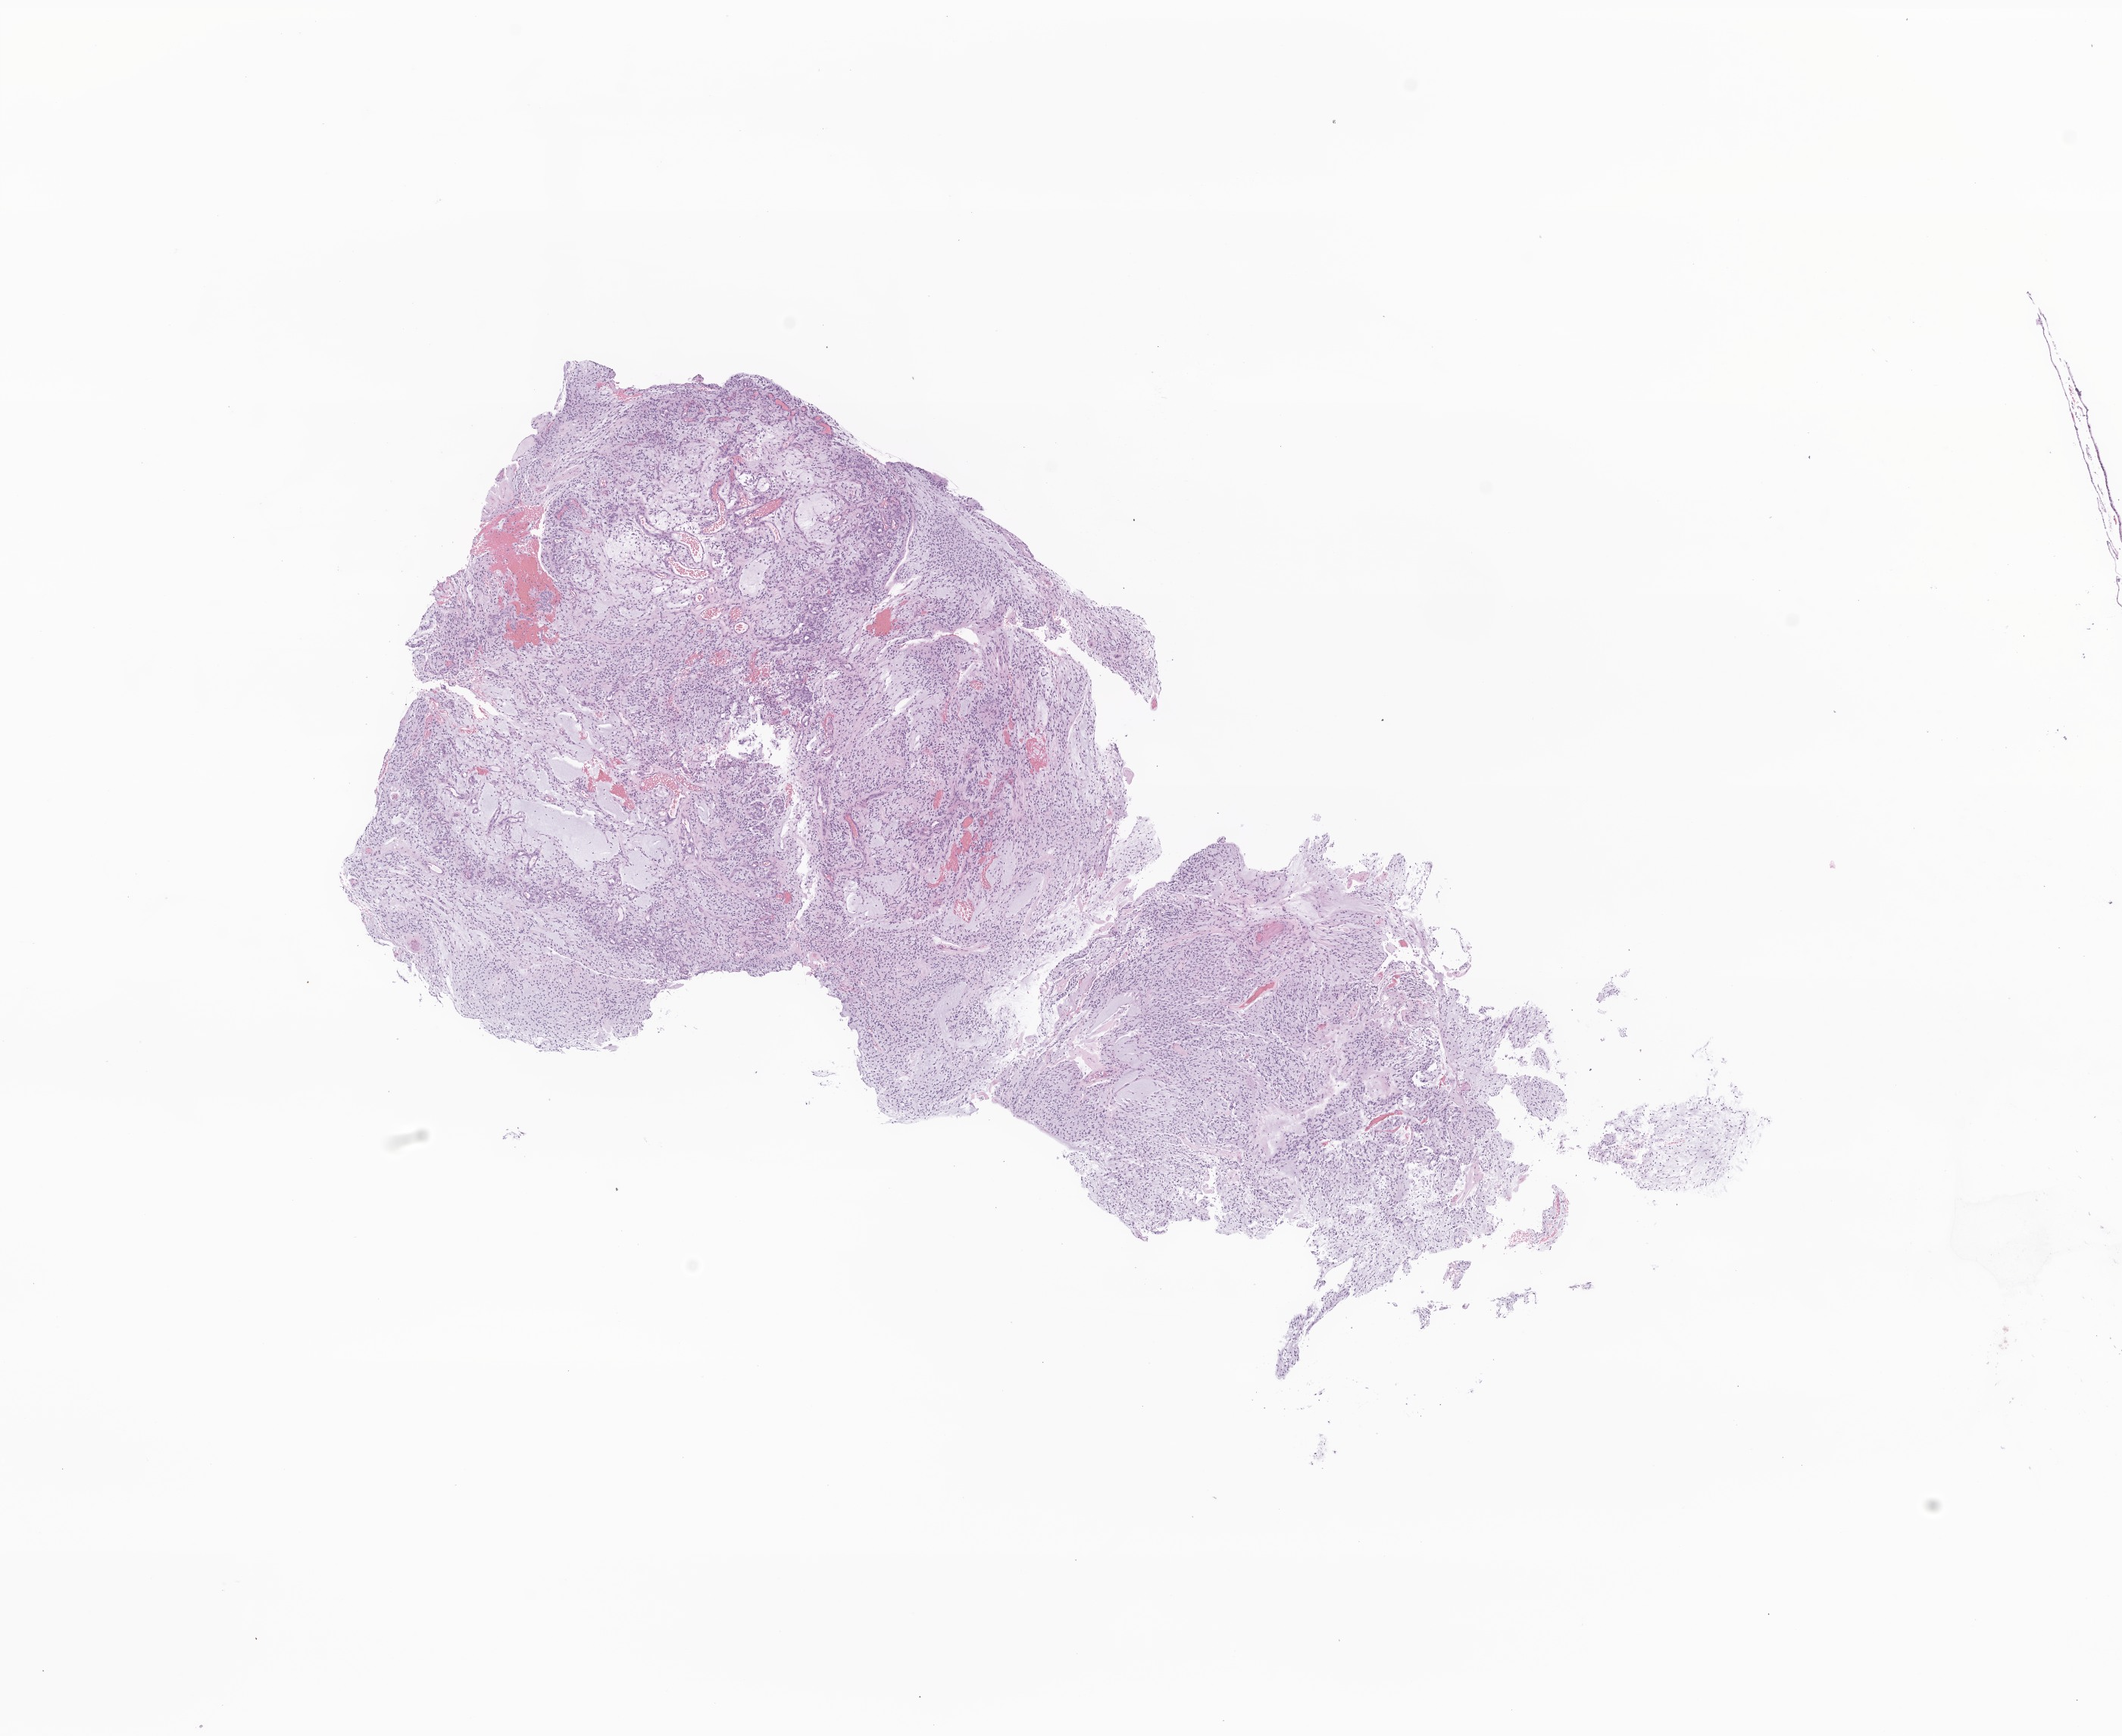
H&E whole-slide image of tumor tissue from the spinal cord — whole scanned area (about 11.8 x 9.7 mm) shown as a low-resolution overview. Formalin-fixed, paraffin-embedded (FFPE) tissue. Female patient, age 40 months (3 years 4 months).
Diagnosis (ICD-O-3 morphology term): Pilocytic astrocytoma.